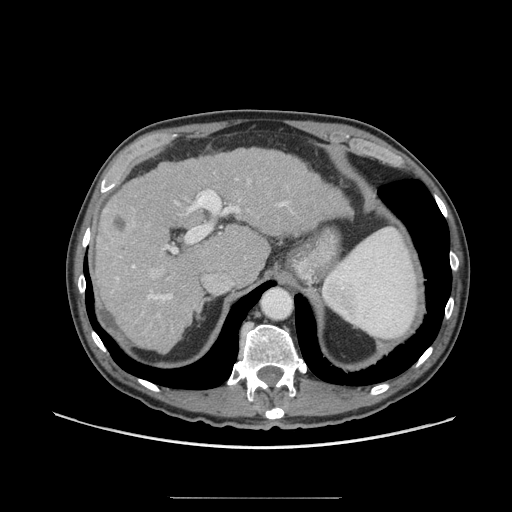
Contrast-enhanced abdominal CT (liver protocol), one axial slice. Slice 48 of 71 in the series (ordered by position). 140 kVp. Soft-tissue window (W 400 / L 40 HU). 2.5 mm slice thickness. 512 × 512 image matrix, field of view 400 × 400 mm. Case-level facts recorded for this patient, not image findings: diagnosis: hepatocellular carcinoma (patient treated with transarterial chemoembolisation; whether this scan precedes or follows treatment is not stated here); TNM stage (as recorded): Stage-I; Child-Pugh class: A; tumour differentiation: well differentiated; tumour nodularity: uninodular.
Structures marked on this image (semi-automatic segmentation, software-assisted and operator-edited):
- liver parenchyma outside the tumour (the mass and vessels are separate outlines, so this box may not span the whole liver): bounding box [x1, y1, x2, y2] px = [94, 148, 350, 352]
- mass: [97, 203, 138, 259]
- liver vessels: [112, 179, 289, 301]